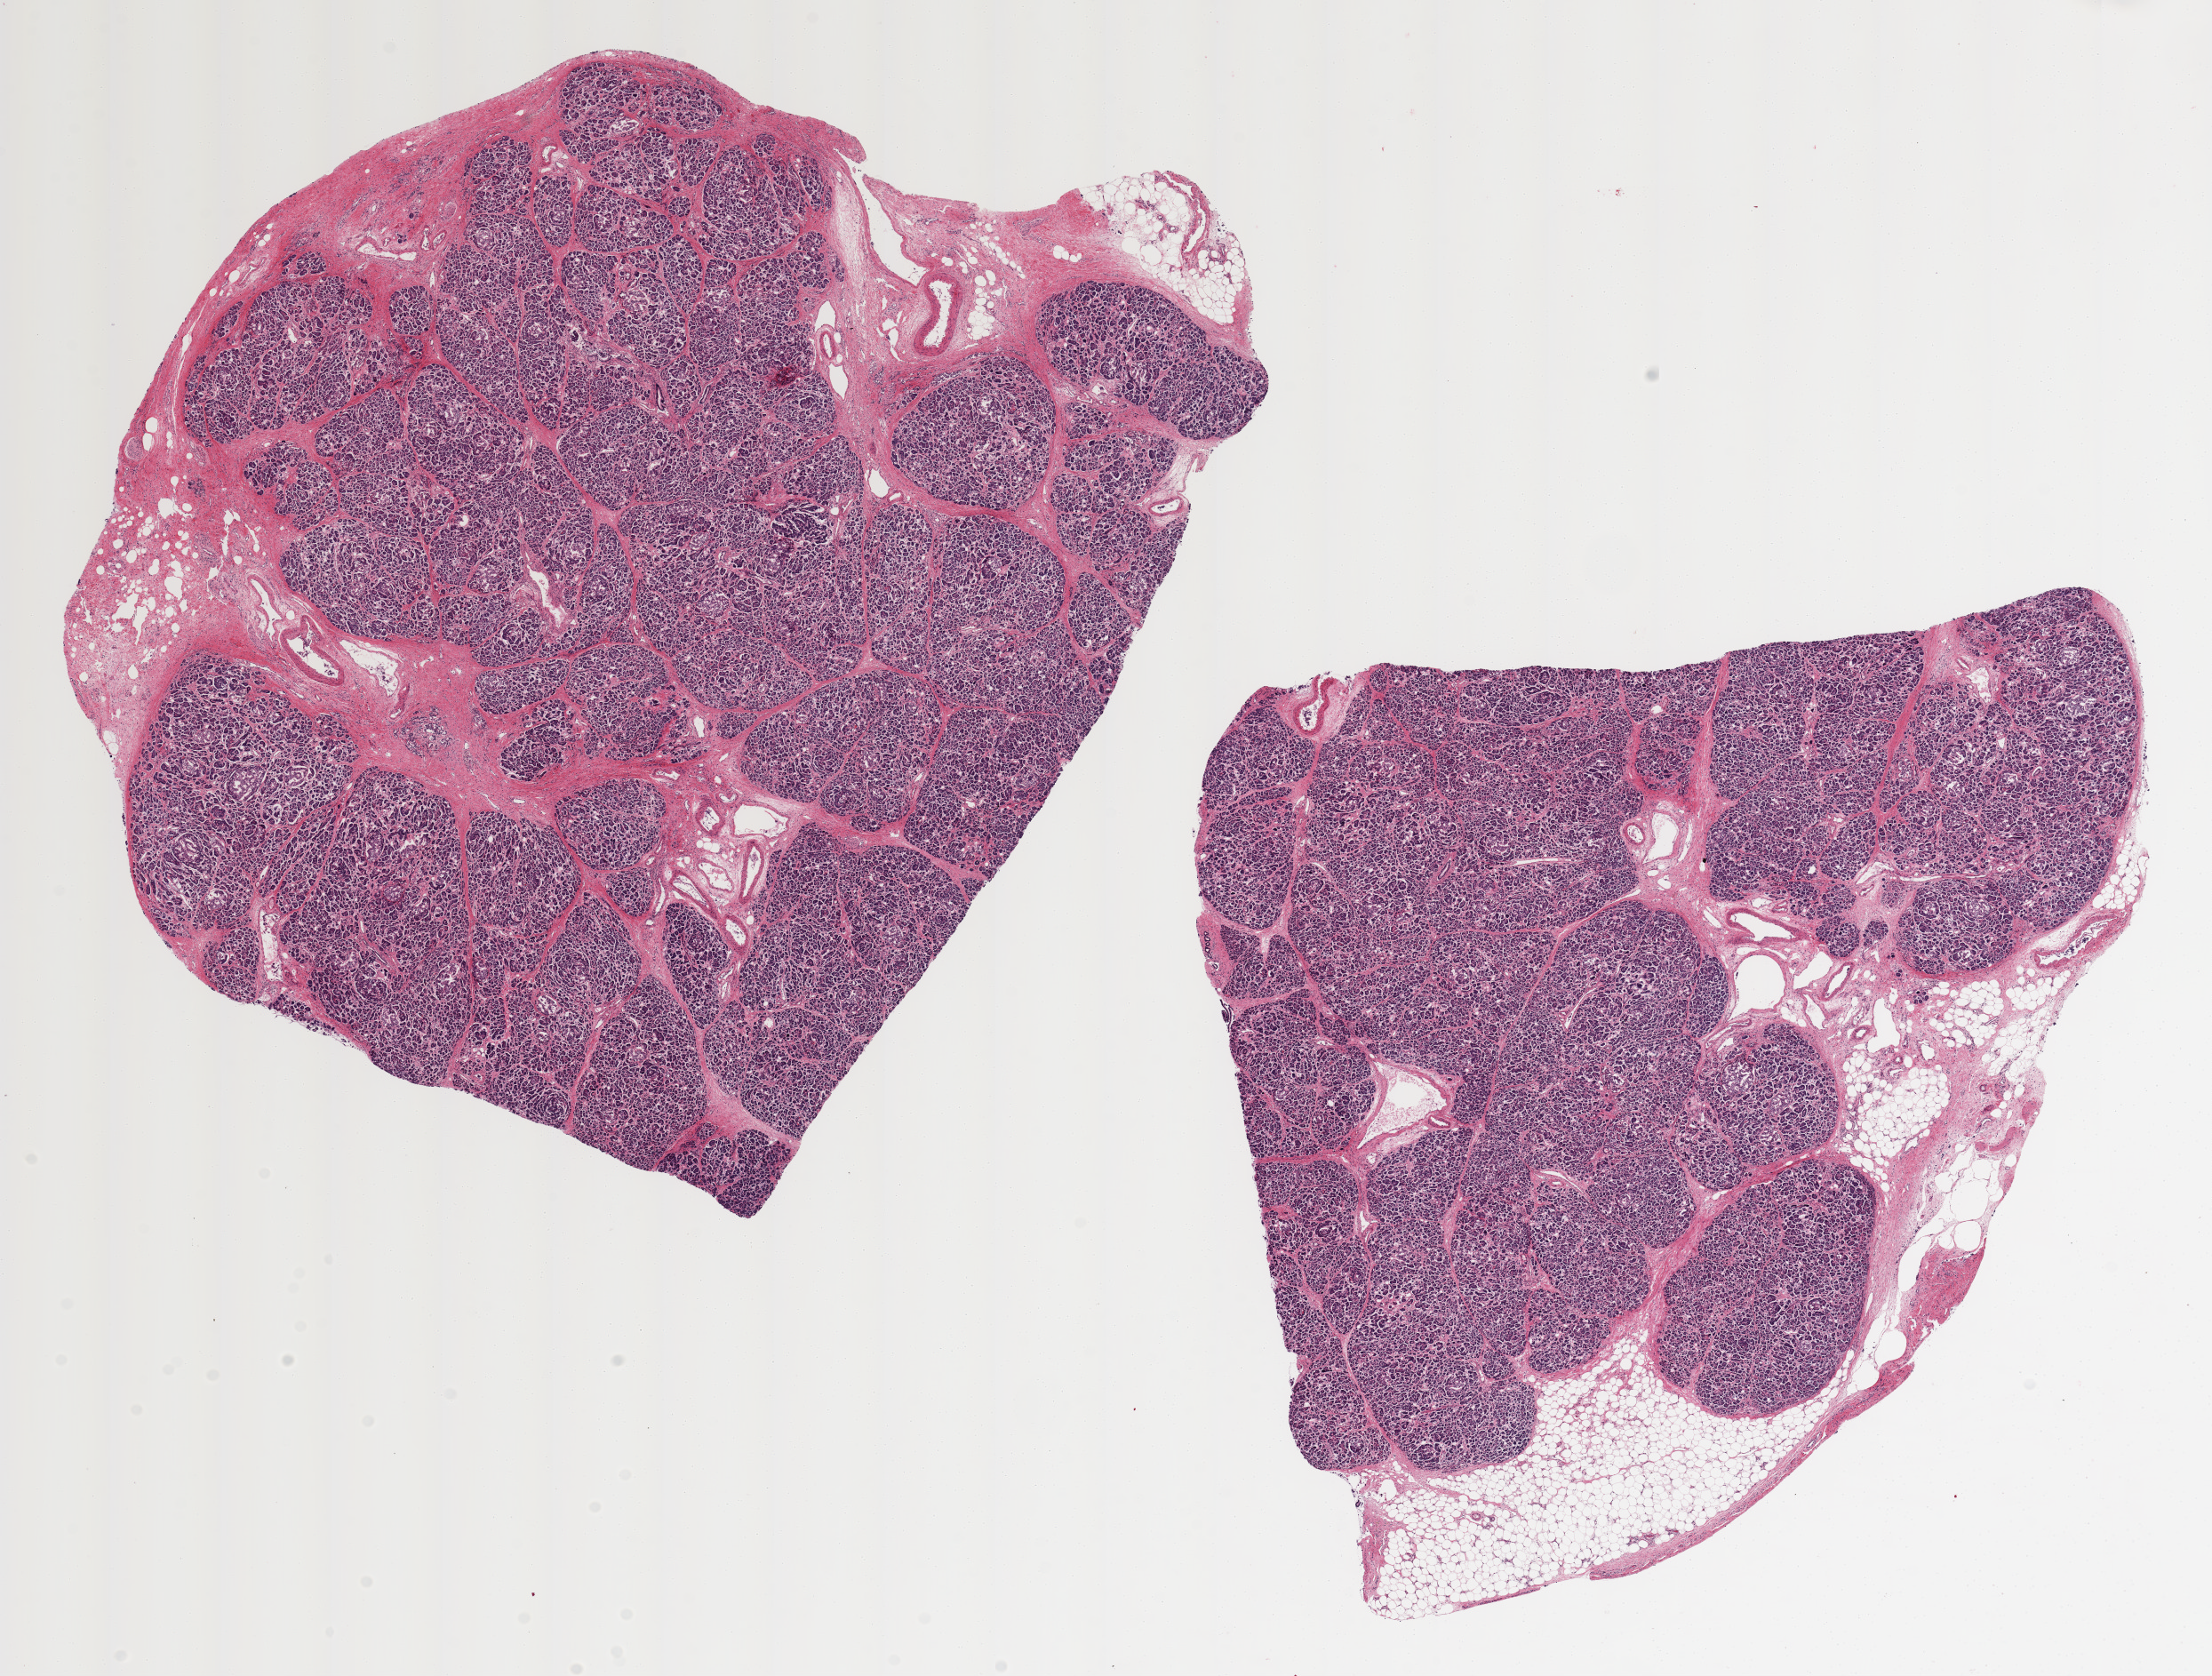
Whole-slide image, haematoxylin and eosin stain, whole scanned area (about 19.7 x 14.9 mm, from a 20x scan) shown as a low-resolution overview. PAXgene-fixed, paraffin-embedded tissue. Target tissue: pancreas. Tissue donor sample.
Reviewer comment on this tissue sample: 2 ~9x9mm aliquots, ~10% adherent fat with saponification.